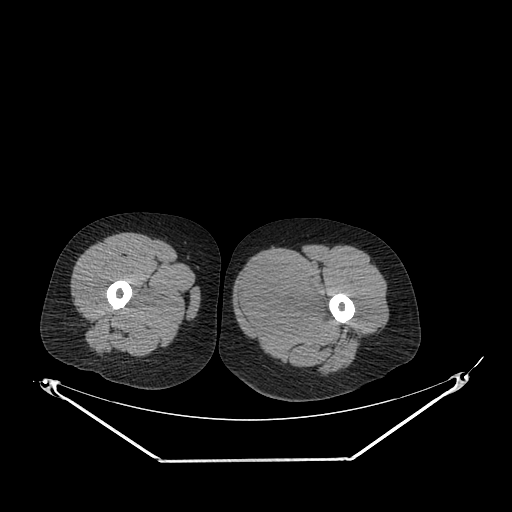
CT of an extremity soft-tissue mass (from a PET/CT study), one axial slice; slice 236 of 267 in the series (ordered by position); reconstruction kernel SOFT; 120 kVp; soft-tissue window (W 400 / L 40 HU); 3.75 mm slice thickness; 512 × 512 image matrix, field of view 500 × 500 mm. Female patient. Case-level facts recorded for this patient, not image findings: histological type: pleiomorphic leiomyosarcoma; grade: intermediate; site of the primary tumour: left thigh.
Annotated regions visible in this slice (expert contour drawn on MRI and transferred to this co-registered scan by the dataset authors):
- gross tumour volume including surrounding oedema: bounding box (x1, y1, x2, y2) in pixels: (237, 260, 330, 332)
- gross tumour volume (mass): (237, 260, 328, 330)